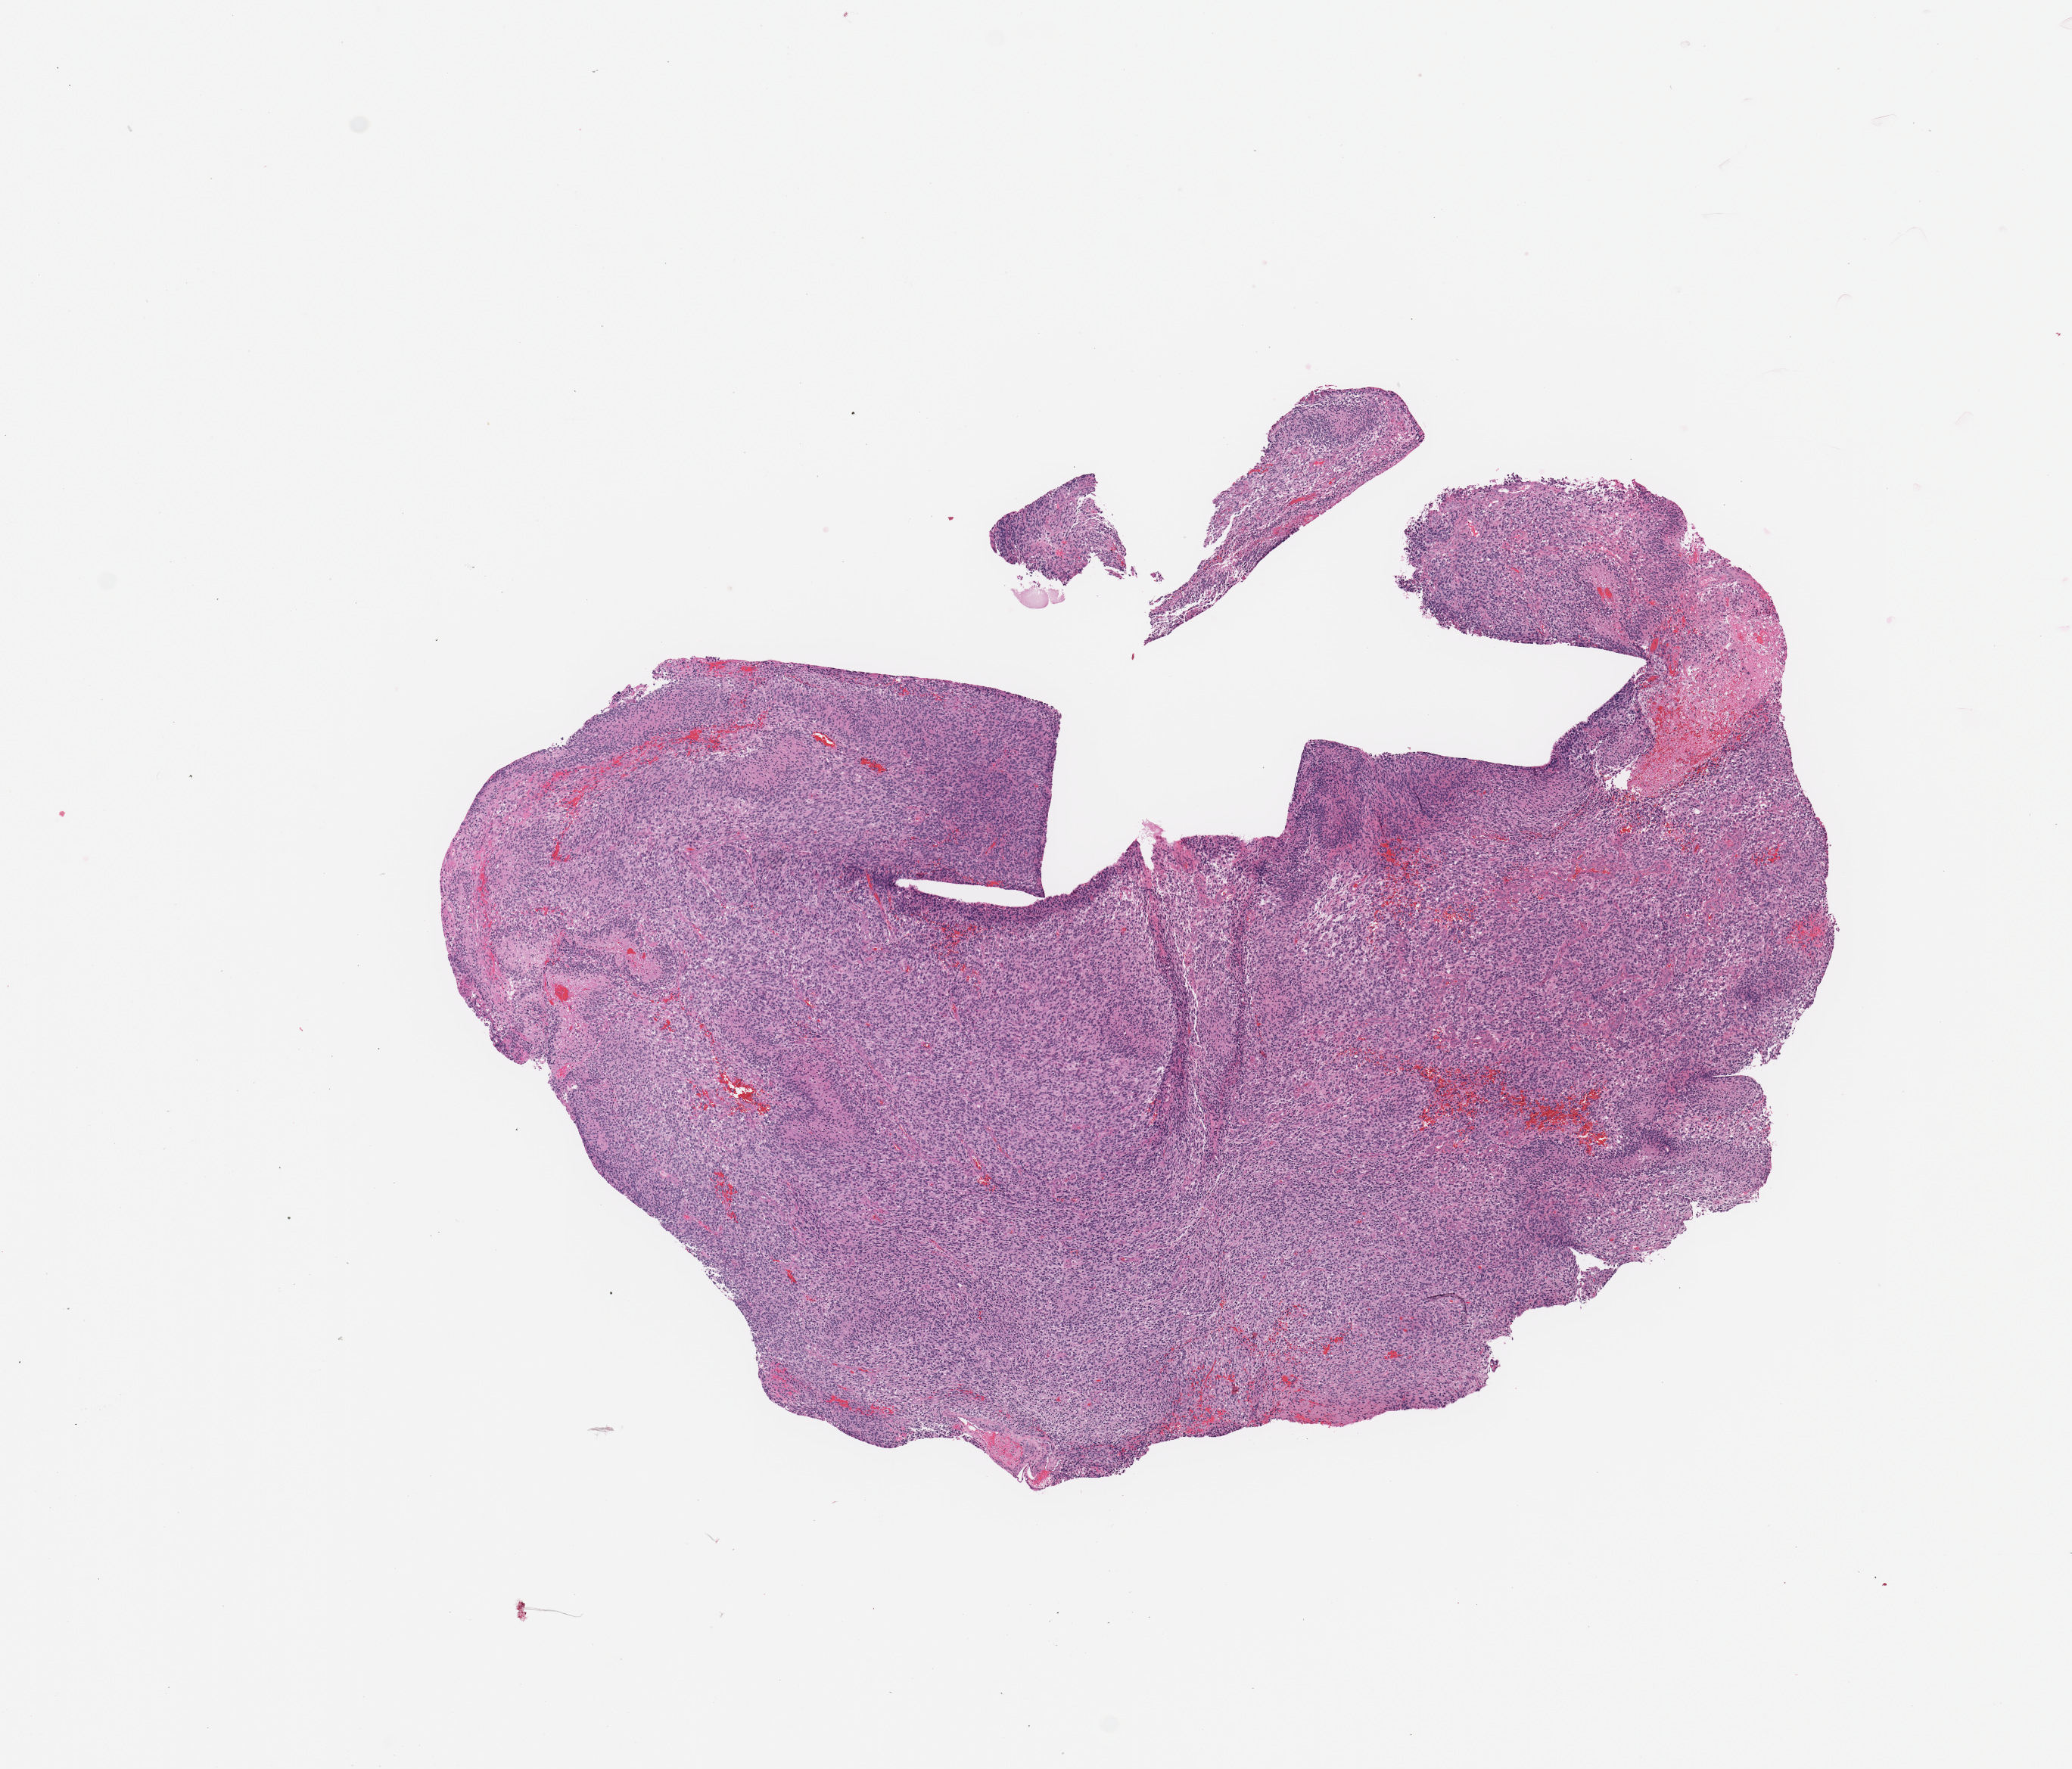
Hematoxylin and eosin (H&E) stained whole-slide image — whole scanned area (about 10.8 x 9.2 mm, from a 20x scan) shown as a low-resolution overview, tumour tissue sample, sampled site: brain. 66-year-old male patient. Slide review estimates, as recorded: tumour nuclei 80%, necrosis 7%.
Histologic diagnosis: Glioblastoma.